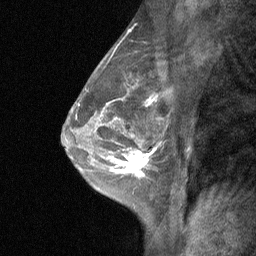
Breast MRI (dynamic contrast-enhanced), one sagittal slice; slice 40 of 64 in the series (ordered by position); dynamic contrast-enhanced study with each time point stored as its own series, time point 2 of 3 at this slice position (early post-contrast, ordered by acquisition time); 1.5 T; TE 4.8 ms, TR 27 ms; 2 mm slice thickness; 256 × 256 image matrix, field of view 180 × 180 mm. Patient: female, 47 years. Case-level facts recorded for this patient, not image findings: setting: breast cancer imaged before/during neoadjuvant chemotherapy; receptor status: HR-positive, HER2-negative.
Outlined on this slice (semi-automatic segmentation, software-assisted and operator-edited):
- analysis volume of interest (the breast-tissue region the enhancement analysis was run in; not a lesion): bounding box (x1, y1, x2, y2) in pixels: (104, 138, 161, 198)
- tumour enhancement mask (voxels above the 90 % enhancement threshold inside the analysis volume of interest): (116, 148, 155, 177)